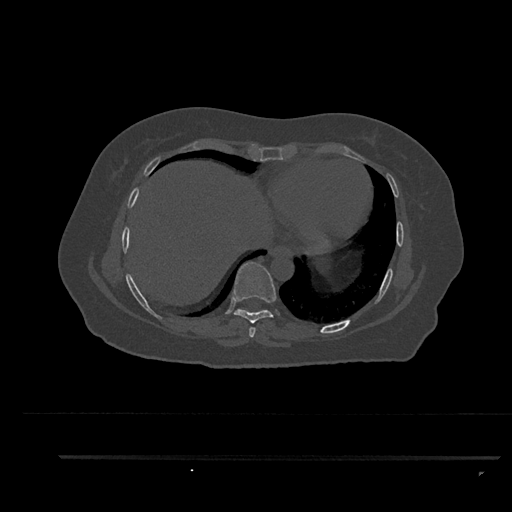
CT including the spine, one axial slice. Slice 454 of 797 in the series (ordered by position). Reconstruction kernel Br40s/3. 120 kVp. Bone window (W 1800 / L 400 HU). 512 × 512 image matrix. Female patient, age 44 years. Case-level facts recorded for this patient, not image findings: primary cancer: renal.
Outlined on this slice (semi-automatic segmentation, software-assisted and operator-edited):
- T7 vertebra: bounding box (x1, y1, x2, y2) in pixels: (249, 327, 256, 338)
- T8 vertebra: (233, 262, 276, 324)
- T9 vertebra: (236, 309, 265, 311)